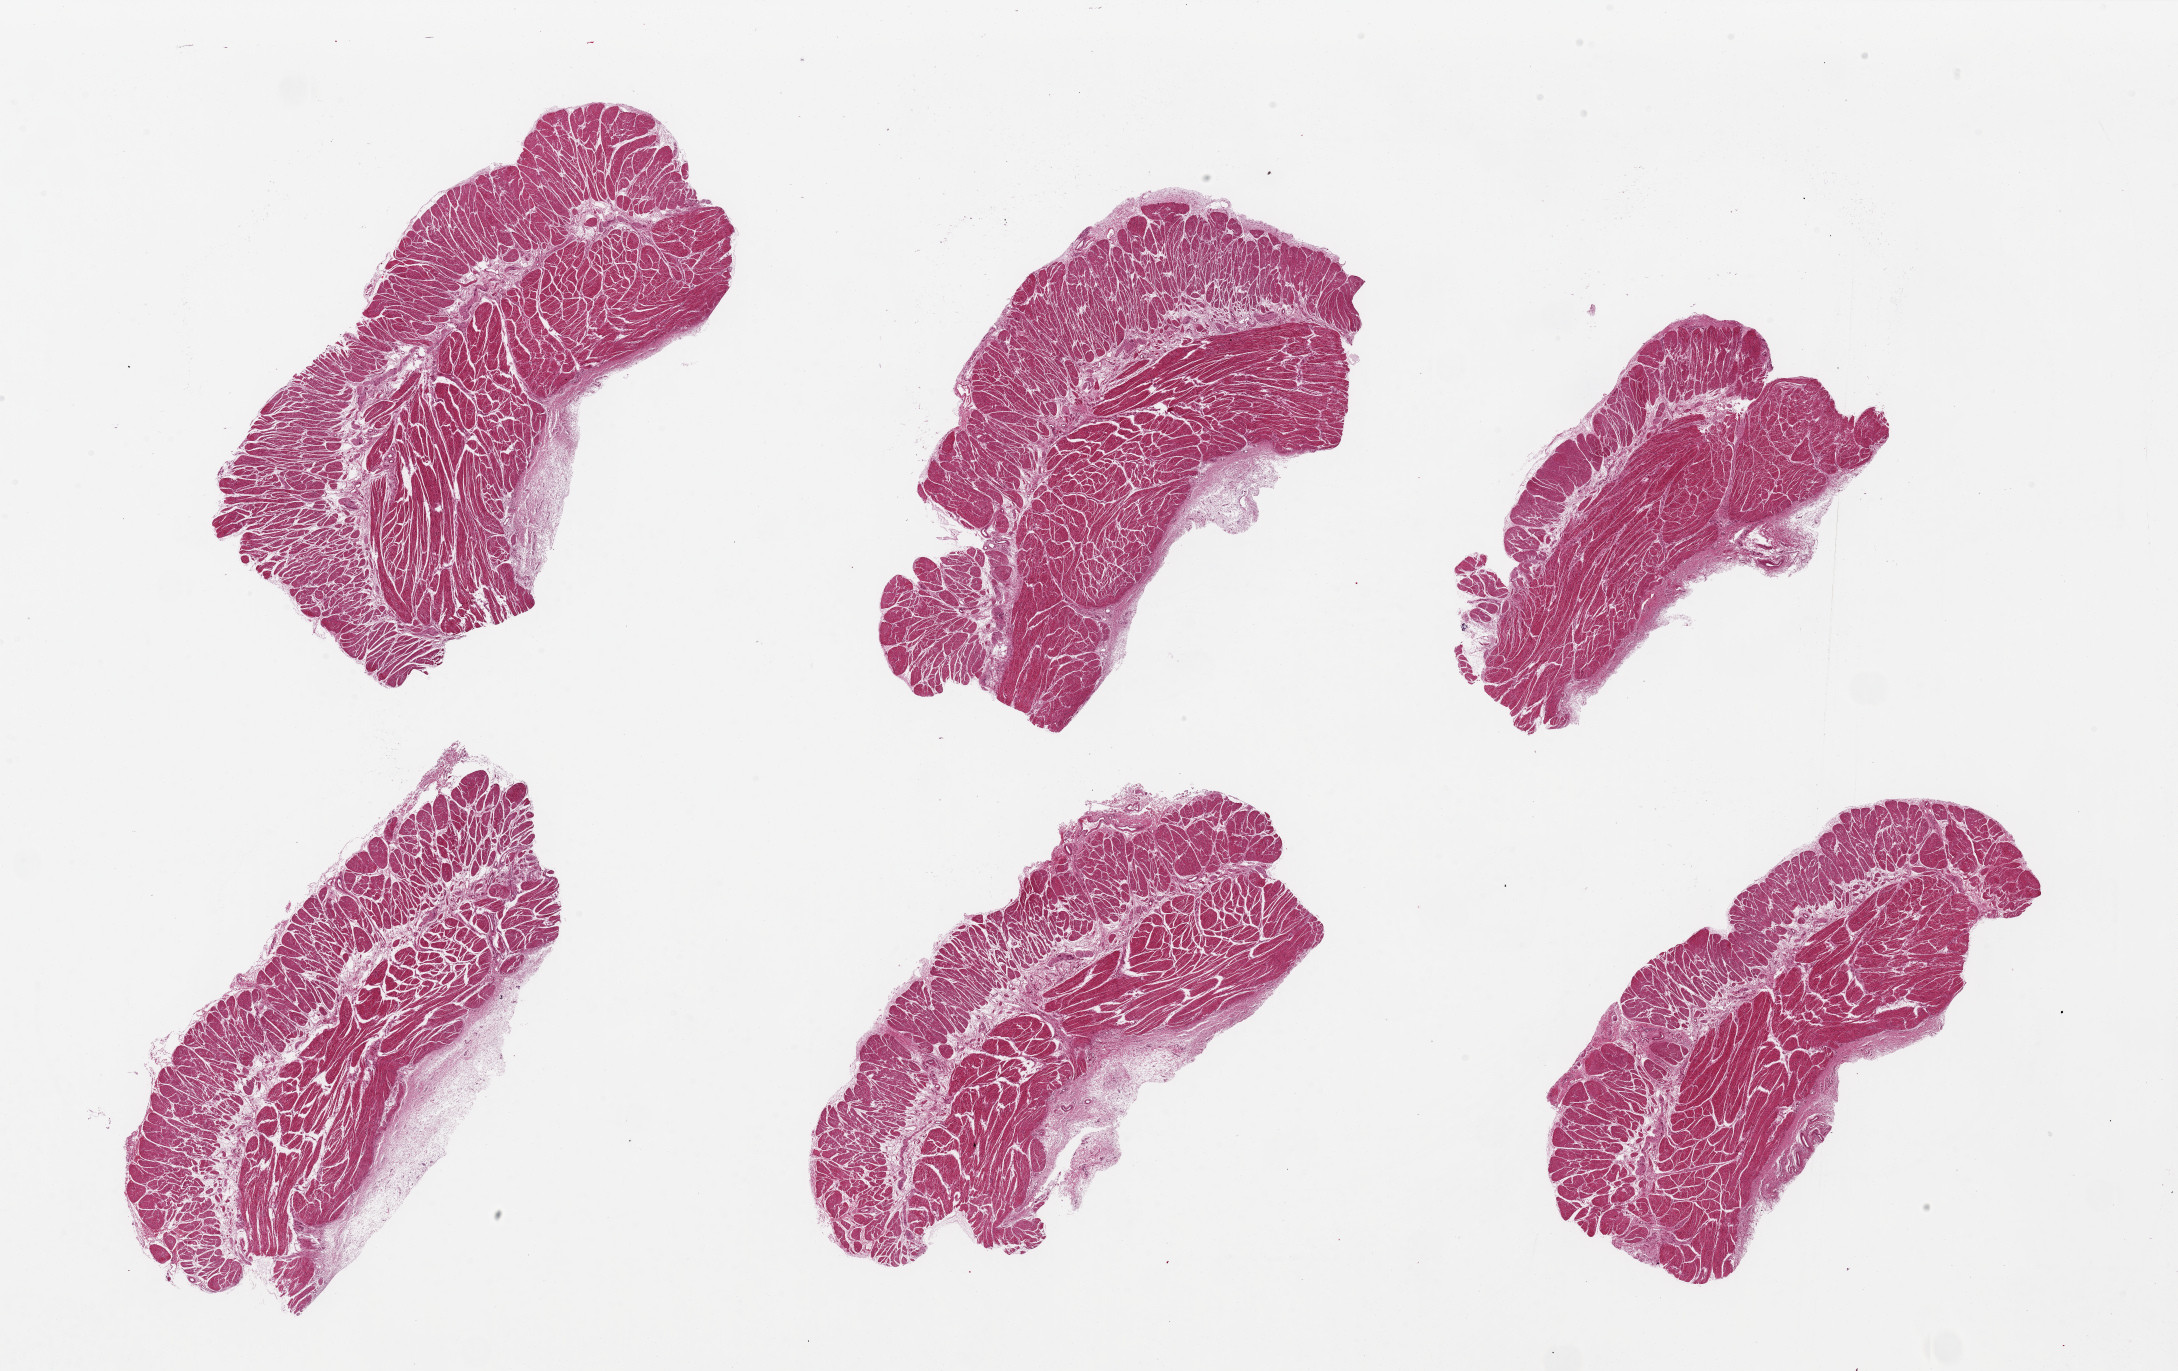
Digitized haematoxylin and eosin-stained section, shown as a low-resolution overview of the whole scanned area (about 34.5 x 21.7 mm, slide scanned at 20x). PAXgene-fixed paraffin-embedded (PFPE) section. Section of esophageal muscle (target tissue). Donor tissue sample.
Reviewer comment on this tissue sample: 6 pieces, up to 10x6mm; all muscularis.